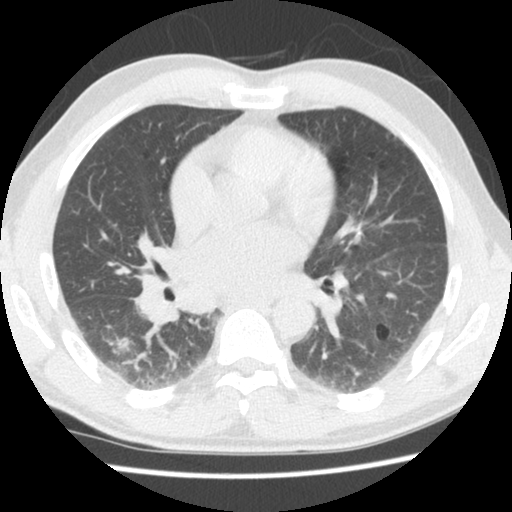
Low-dose screening chest CT, one axial slice; slice 75 of 133 in the series (ordered by position); 140 kVp; lung window (W 1500 / L -600 HU); 2.5 mm slice thickness; 512 × 512 image matrix, field of view 320 × 320 mm.
Annotated regions visible in this slice (expert manual segmentation):
- lesion 1 (tumor, lower lobe of right lung): bounding box (x1, y1, x2, y2) in pixels: (114, 337, 133, 356)